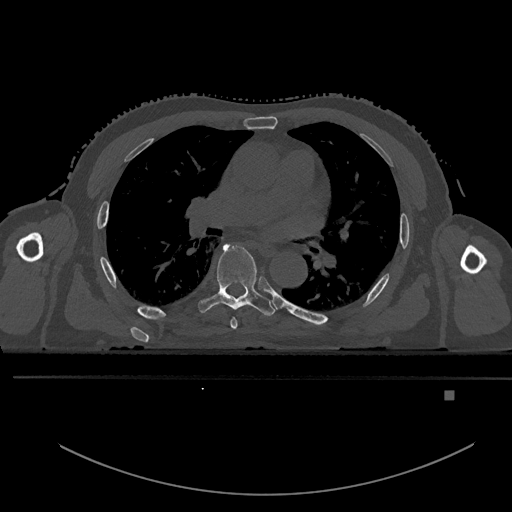
CT including the spine, one axial slice; position 315 of 969 along the scan axis; bone window (W 1800 / L 400 HU); 0.5 mm slice thickness; 512 × 512 image matrix, field of view 456 × 456 mm. Male patient, age 82 years. Case-level facts recorded for this patient, not image findings: primary cancer: prostate.
Structures marked on this image (semi-automatic segmentation, software-assisted and operator-edited):
- T5 vertebra: box from (x=230, y=317) to (x=238, y=330) px
- T6 vertebra: (x=198, y=244)–(x=276, y=317)